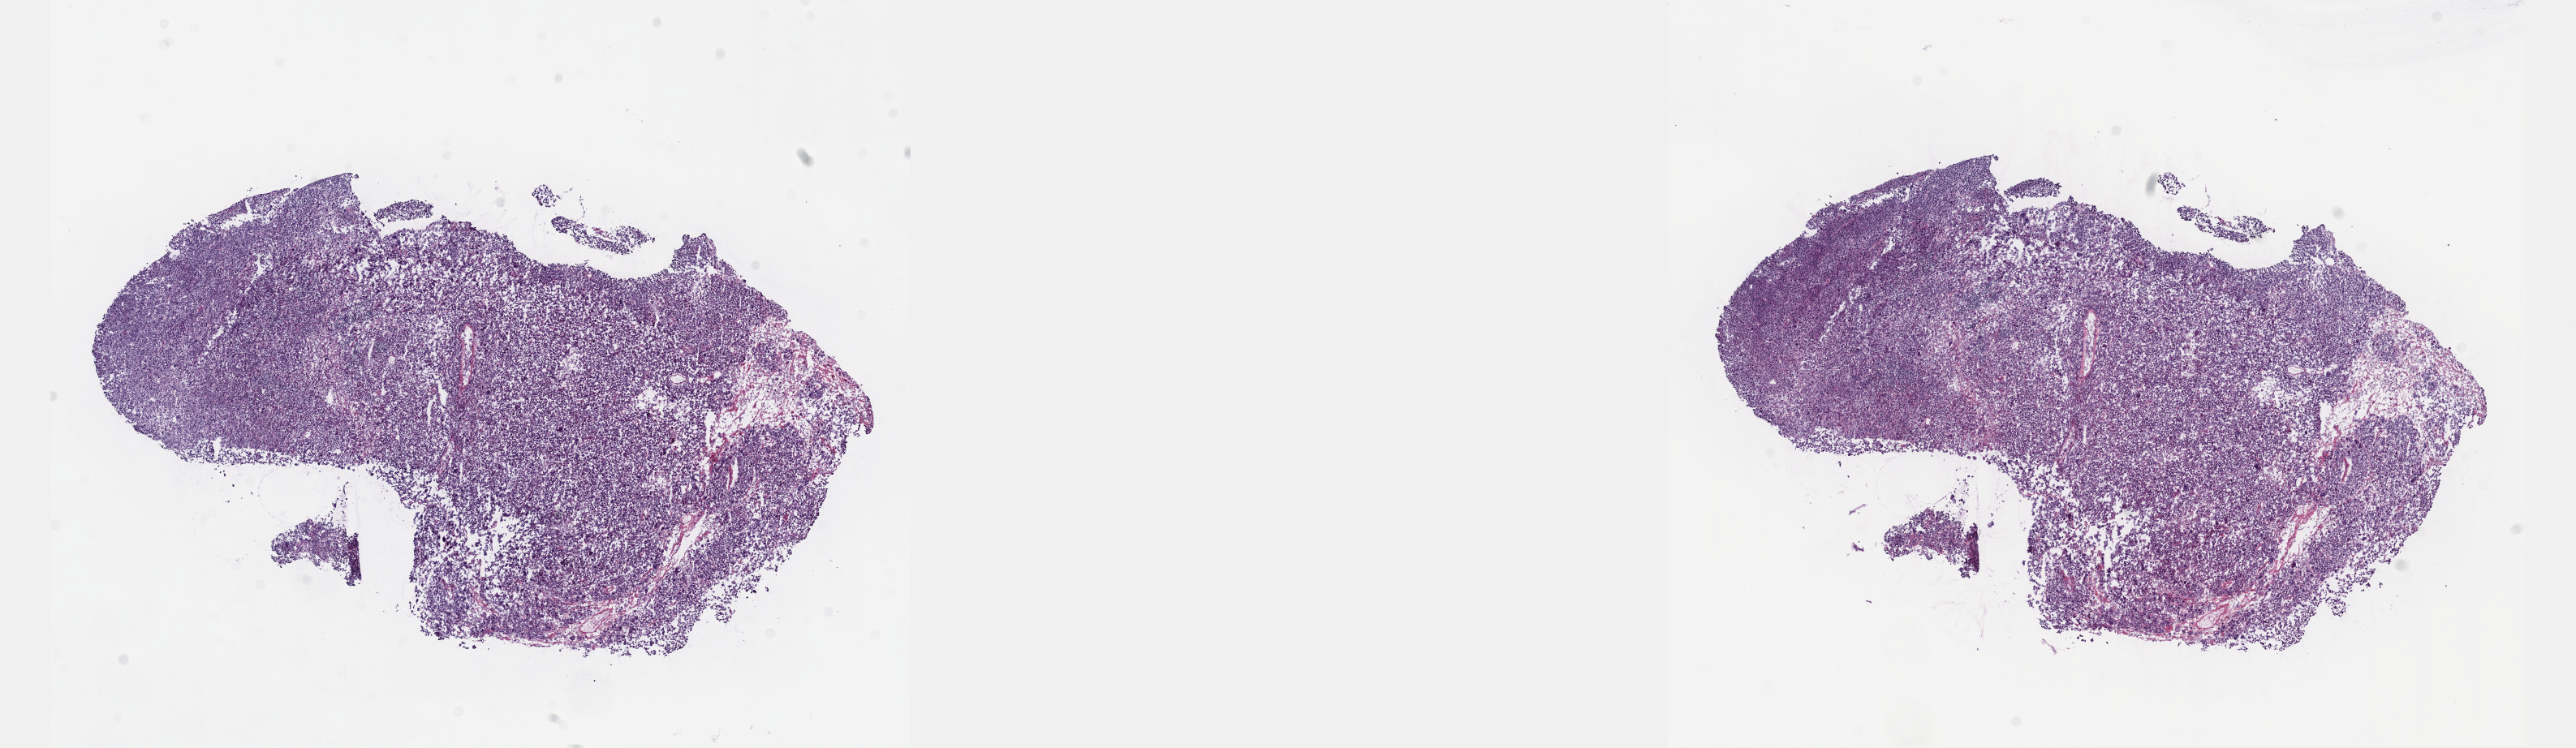
Digitized Hematoxylin and eosin (H&E) stained tissue section (whole slide) — low-resolution overview of the scanned area, about 25.7 x 7.5 mm. Frozen section from the top of the tissue portion. Metastatic tumour sample. Male patient; age at initial diagnosis 49 years. Composition of this section per pathologist review: tumour cells 85%, tumour nuclei 85%, normal cells 0%, stromal cells 14%, necrosis 1%. Inflammatory infiltration, as recorded: lymphocyte infiltration 4%, monocyte infiltration 1%, neutrophil infiltration 1%.
This section: metastatic tumour tissue. Patient diagnosis: Nodular melanoma.